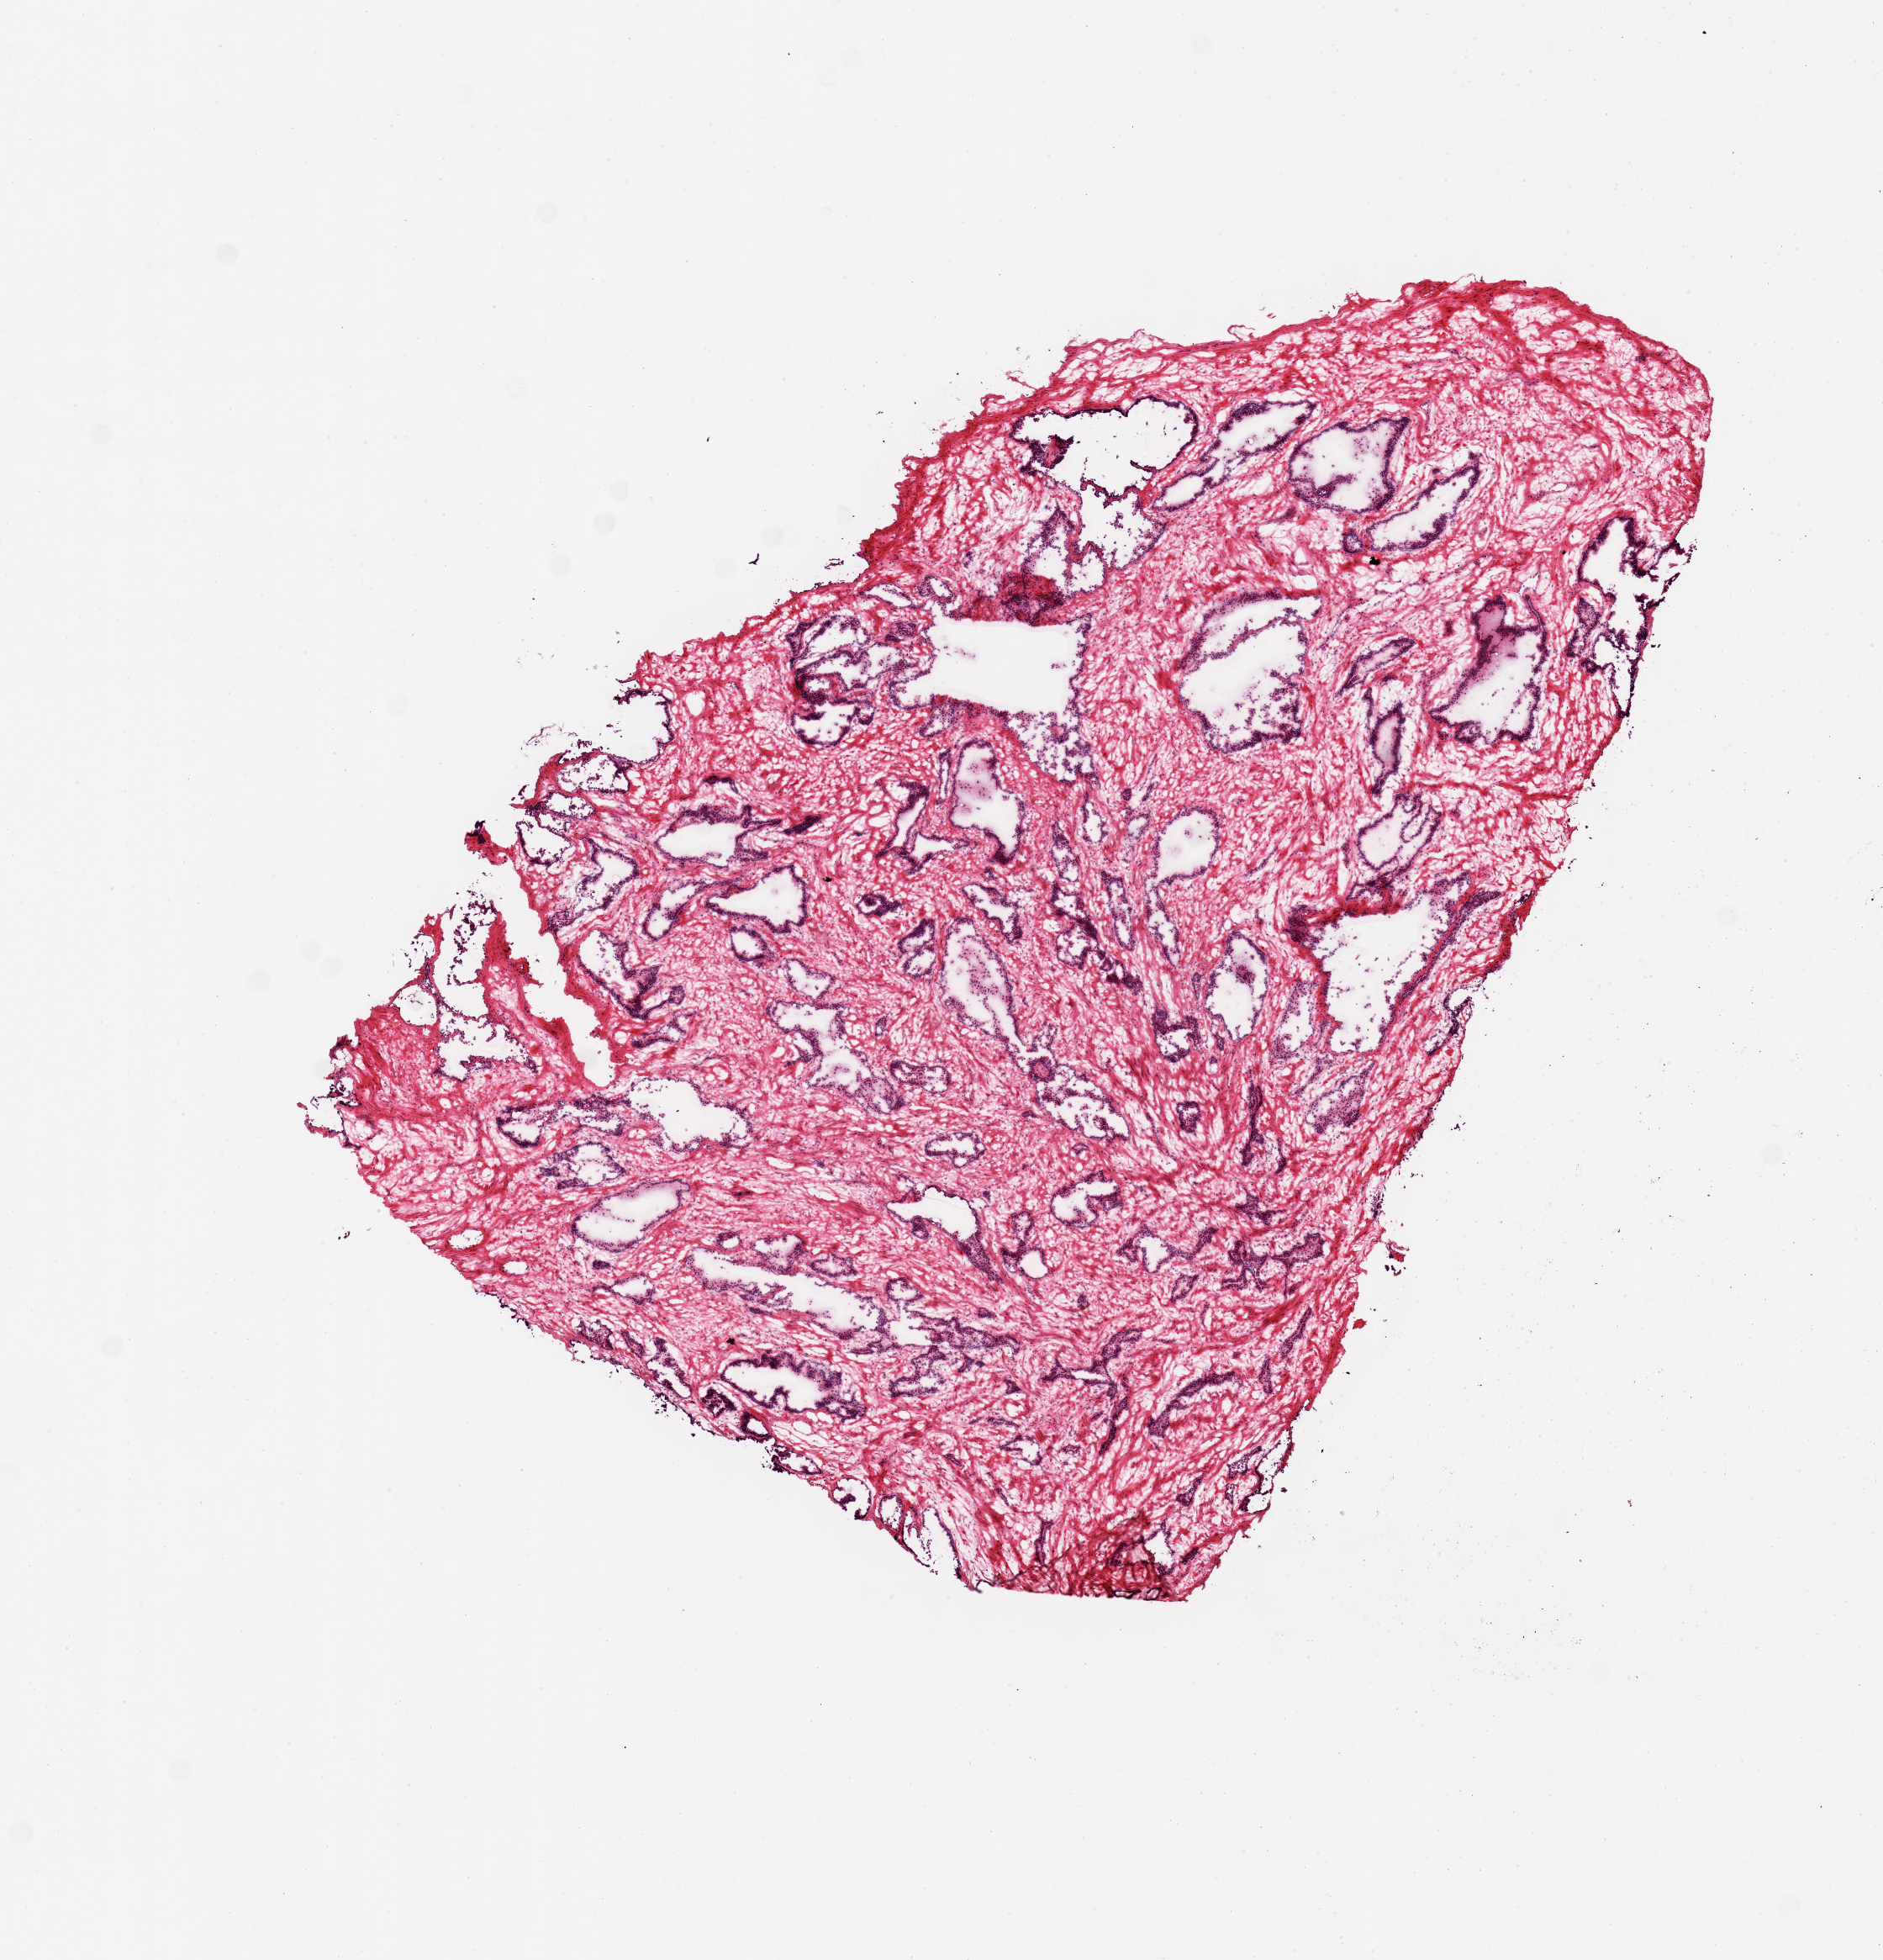
Whole-slide image, hematoxylin and eosin (H&E) stain, whole scanned area (about 8.9 x 9.2 mm) shown as a low-resolution overview; frozen section; sampled site (target tissue): prostate; tissue donor sample. Donor sex: male.
Pathologist's review note for this sample: 1 piece; good prostatic tissue, but unacceptable based on PAXgene unacceptability.